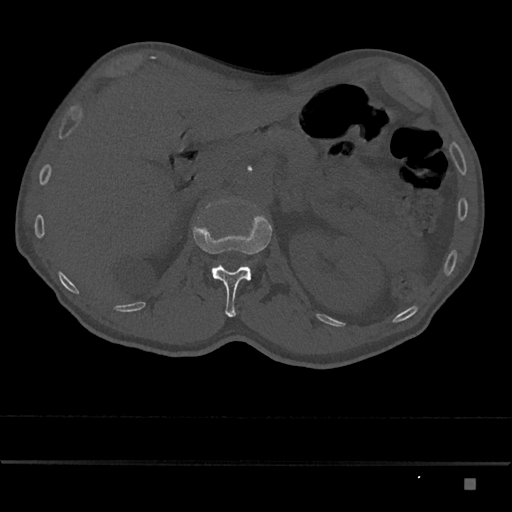
CT including the spine, one axial slice. Slice 533 of 797 in the series (ordered by position). Reconstruction kernel Br40s/3. Bone window (W 1800 / L 400 HU). 0.5 mm slice thickness. 512 × 512 image matrix, field of view 390 × 390 mm. Male patient, age 72 years. Case-level facts recorded for this patient, not image findings: primary cancer: prostate.
Annotated regions visible in this slice (semi-automatic segmentation, software-assisted and operator-edited):
- L1 vertebra: bounding box (x1, y1, x2, y2) in pixels: (192, 216, 272, 317)